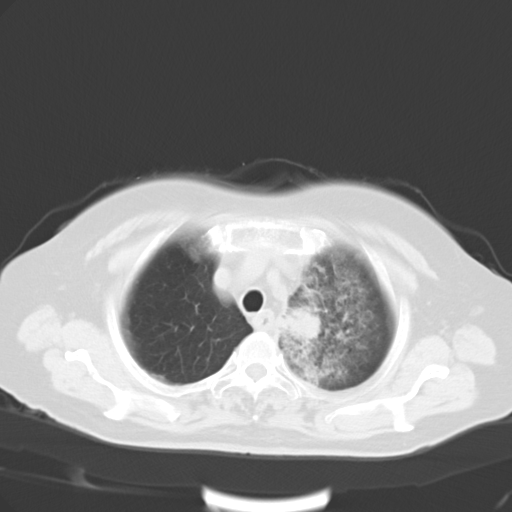
Chest CT, one axial slice; 120 kVp; lung window (W 1500 / L -600 HU); 512 × 512 image matrix, field of view 353 × 353 mm. Patient: female, 65 years. From the clinical record (not read from this slice): clinical TNM (as recorded): T2b N1 M0.
Outlined on this slice (bounding box drawn by a radiologist):
- lung tumour (recorded histology: adenocarcinoma): bounding box (x1, y1, x2, y2) in pixels: (280, 301, 322, 345)